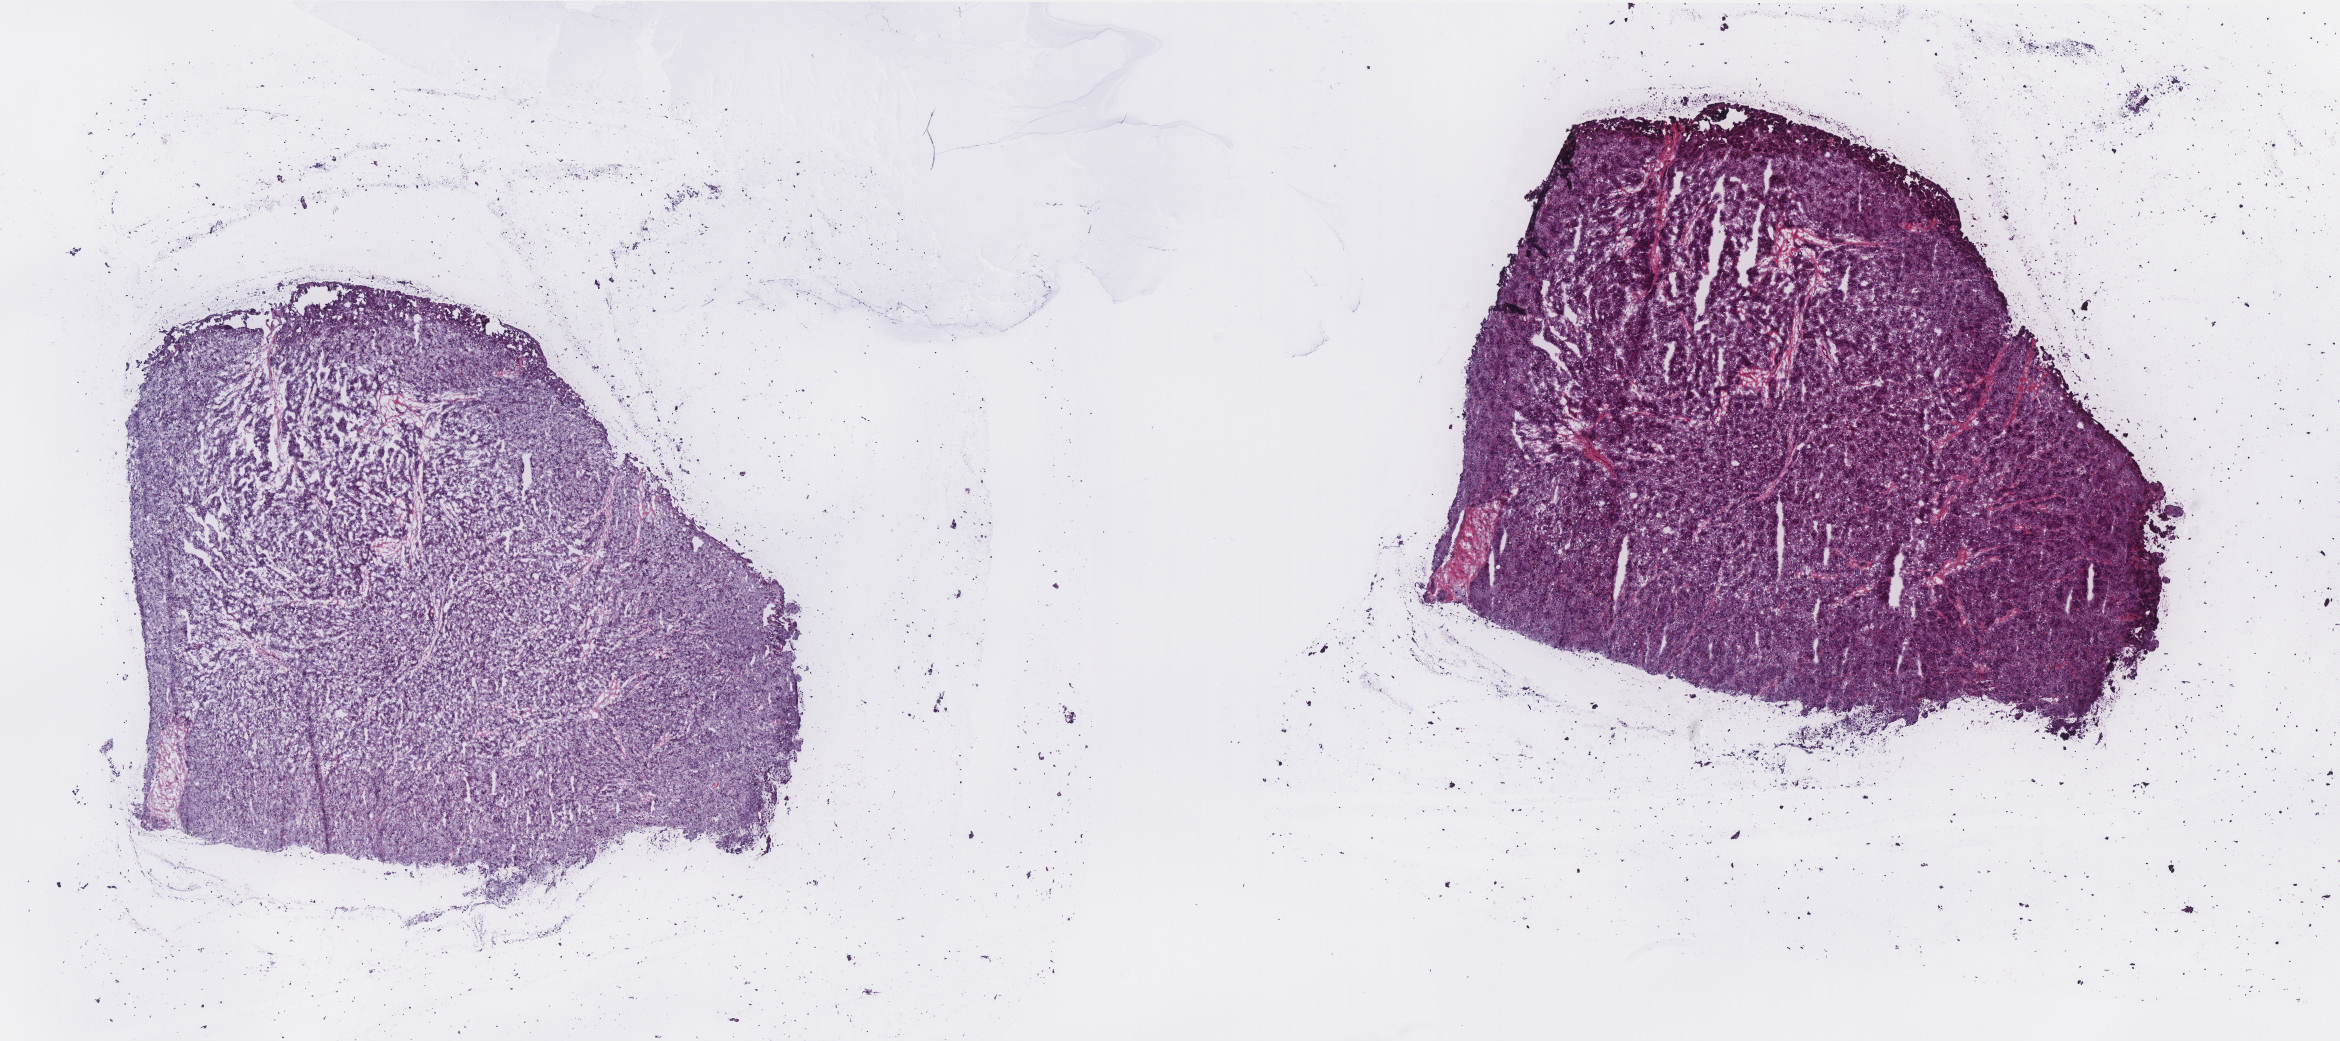
Digitized Hematoxylin and eosin (H&E) stained tissue section (whole slide), shown as a low-resolution overview of the whole scanned area (about 18.8 x 8.3 mm, slide scanned at 40x). Frozen section from the top of the tissue portion. Primary tumour sample from the liver. Male patient; age at initial diagnosis 70 years. Histologic grade: G2 (moderately differentiated). Composition of this section per pathologist review: tumour cells 100%, tumour nuclei 95%, normal cells 0%, stromal cells 0%, necrosis 0%. Inflammatory infiltration, as recorded: lymphocyte infiltration 0%, monocyte infiltration 0%, neutrophil infiltration 0%.
* TNM: T1 N0 M0
* pathologic diagnosis: Hepatocellular carcinoma, NOS
* AJCC pathologic stage: I (5th edition)